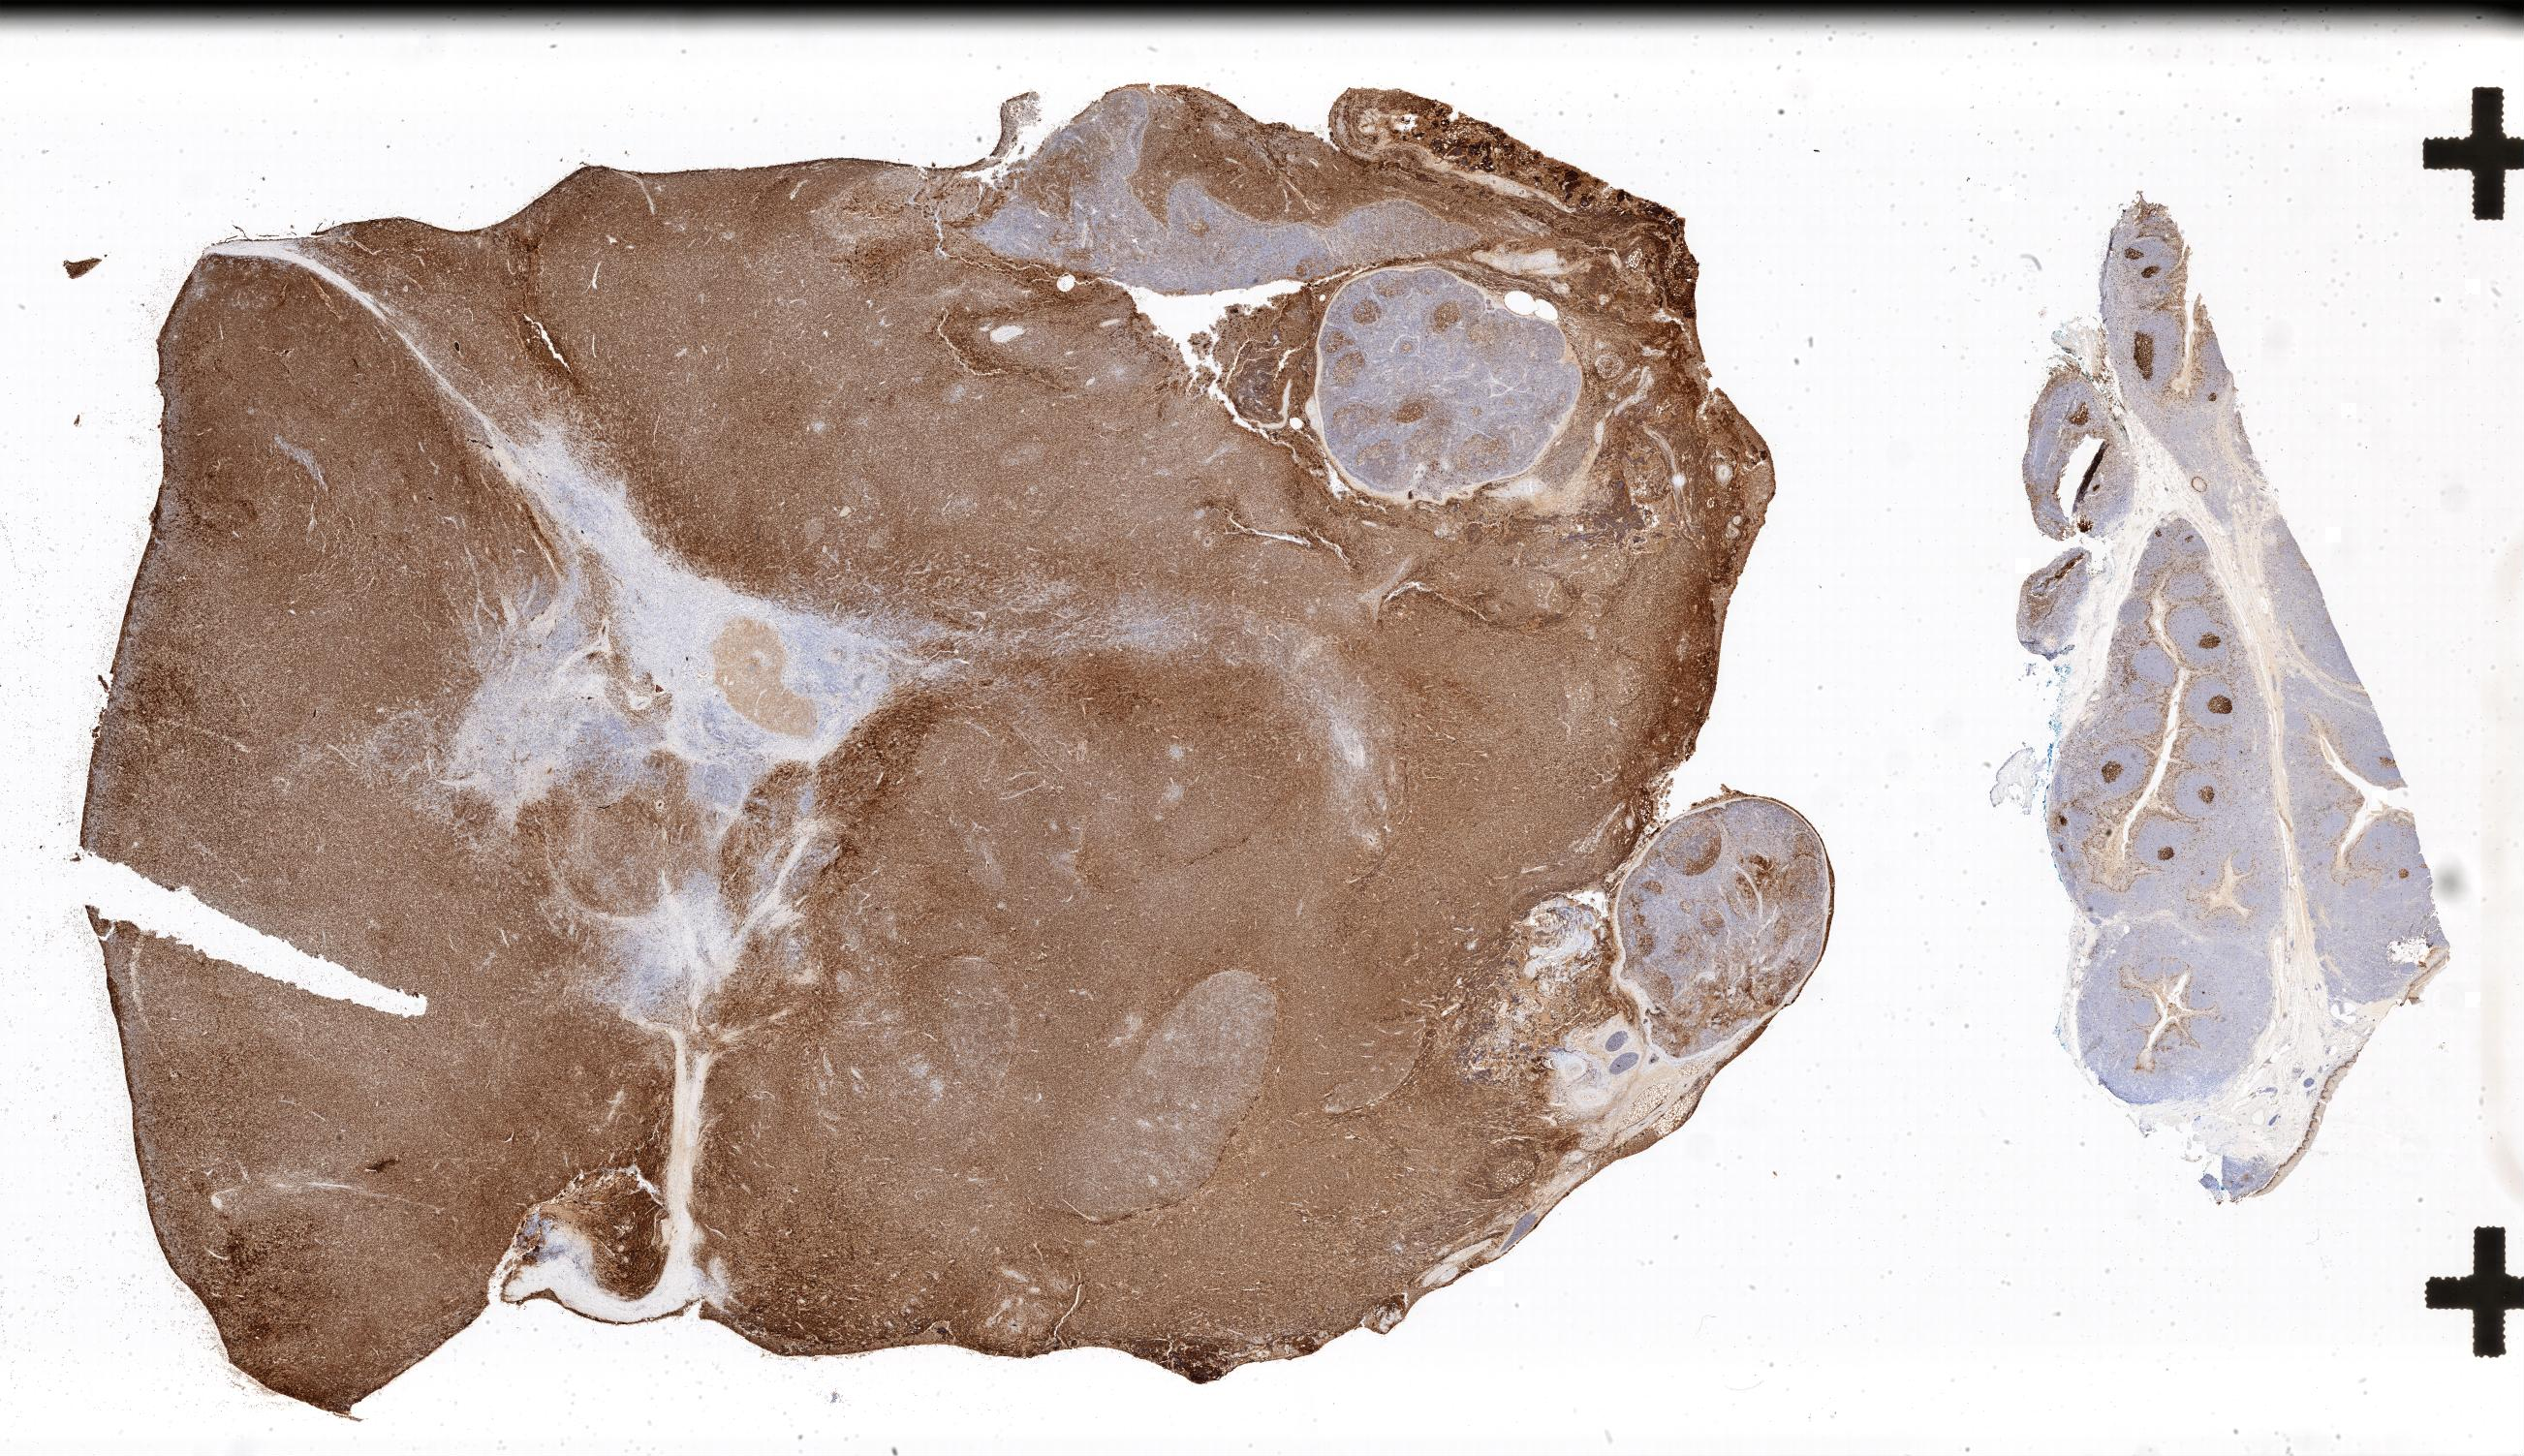
IHC for Ki-67, whole-slide image — shown as a low-resolution overview of the whole scanned area; specimen: tumor tissue; site: lymph node of head and neck. Male patient; age at initial diagnosis 3 years.
Histologic diagnosis: Burkitt lymphoma, NOS.